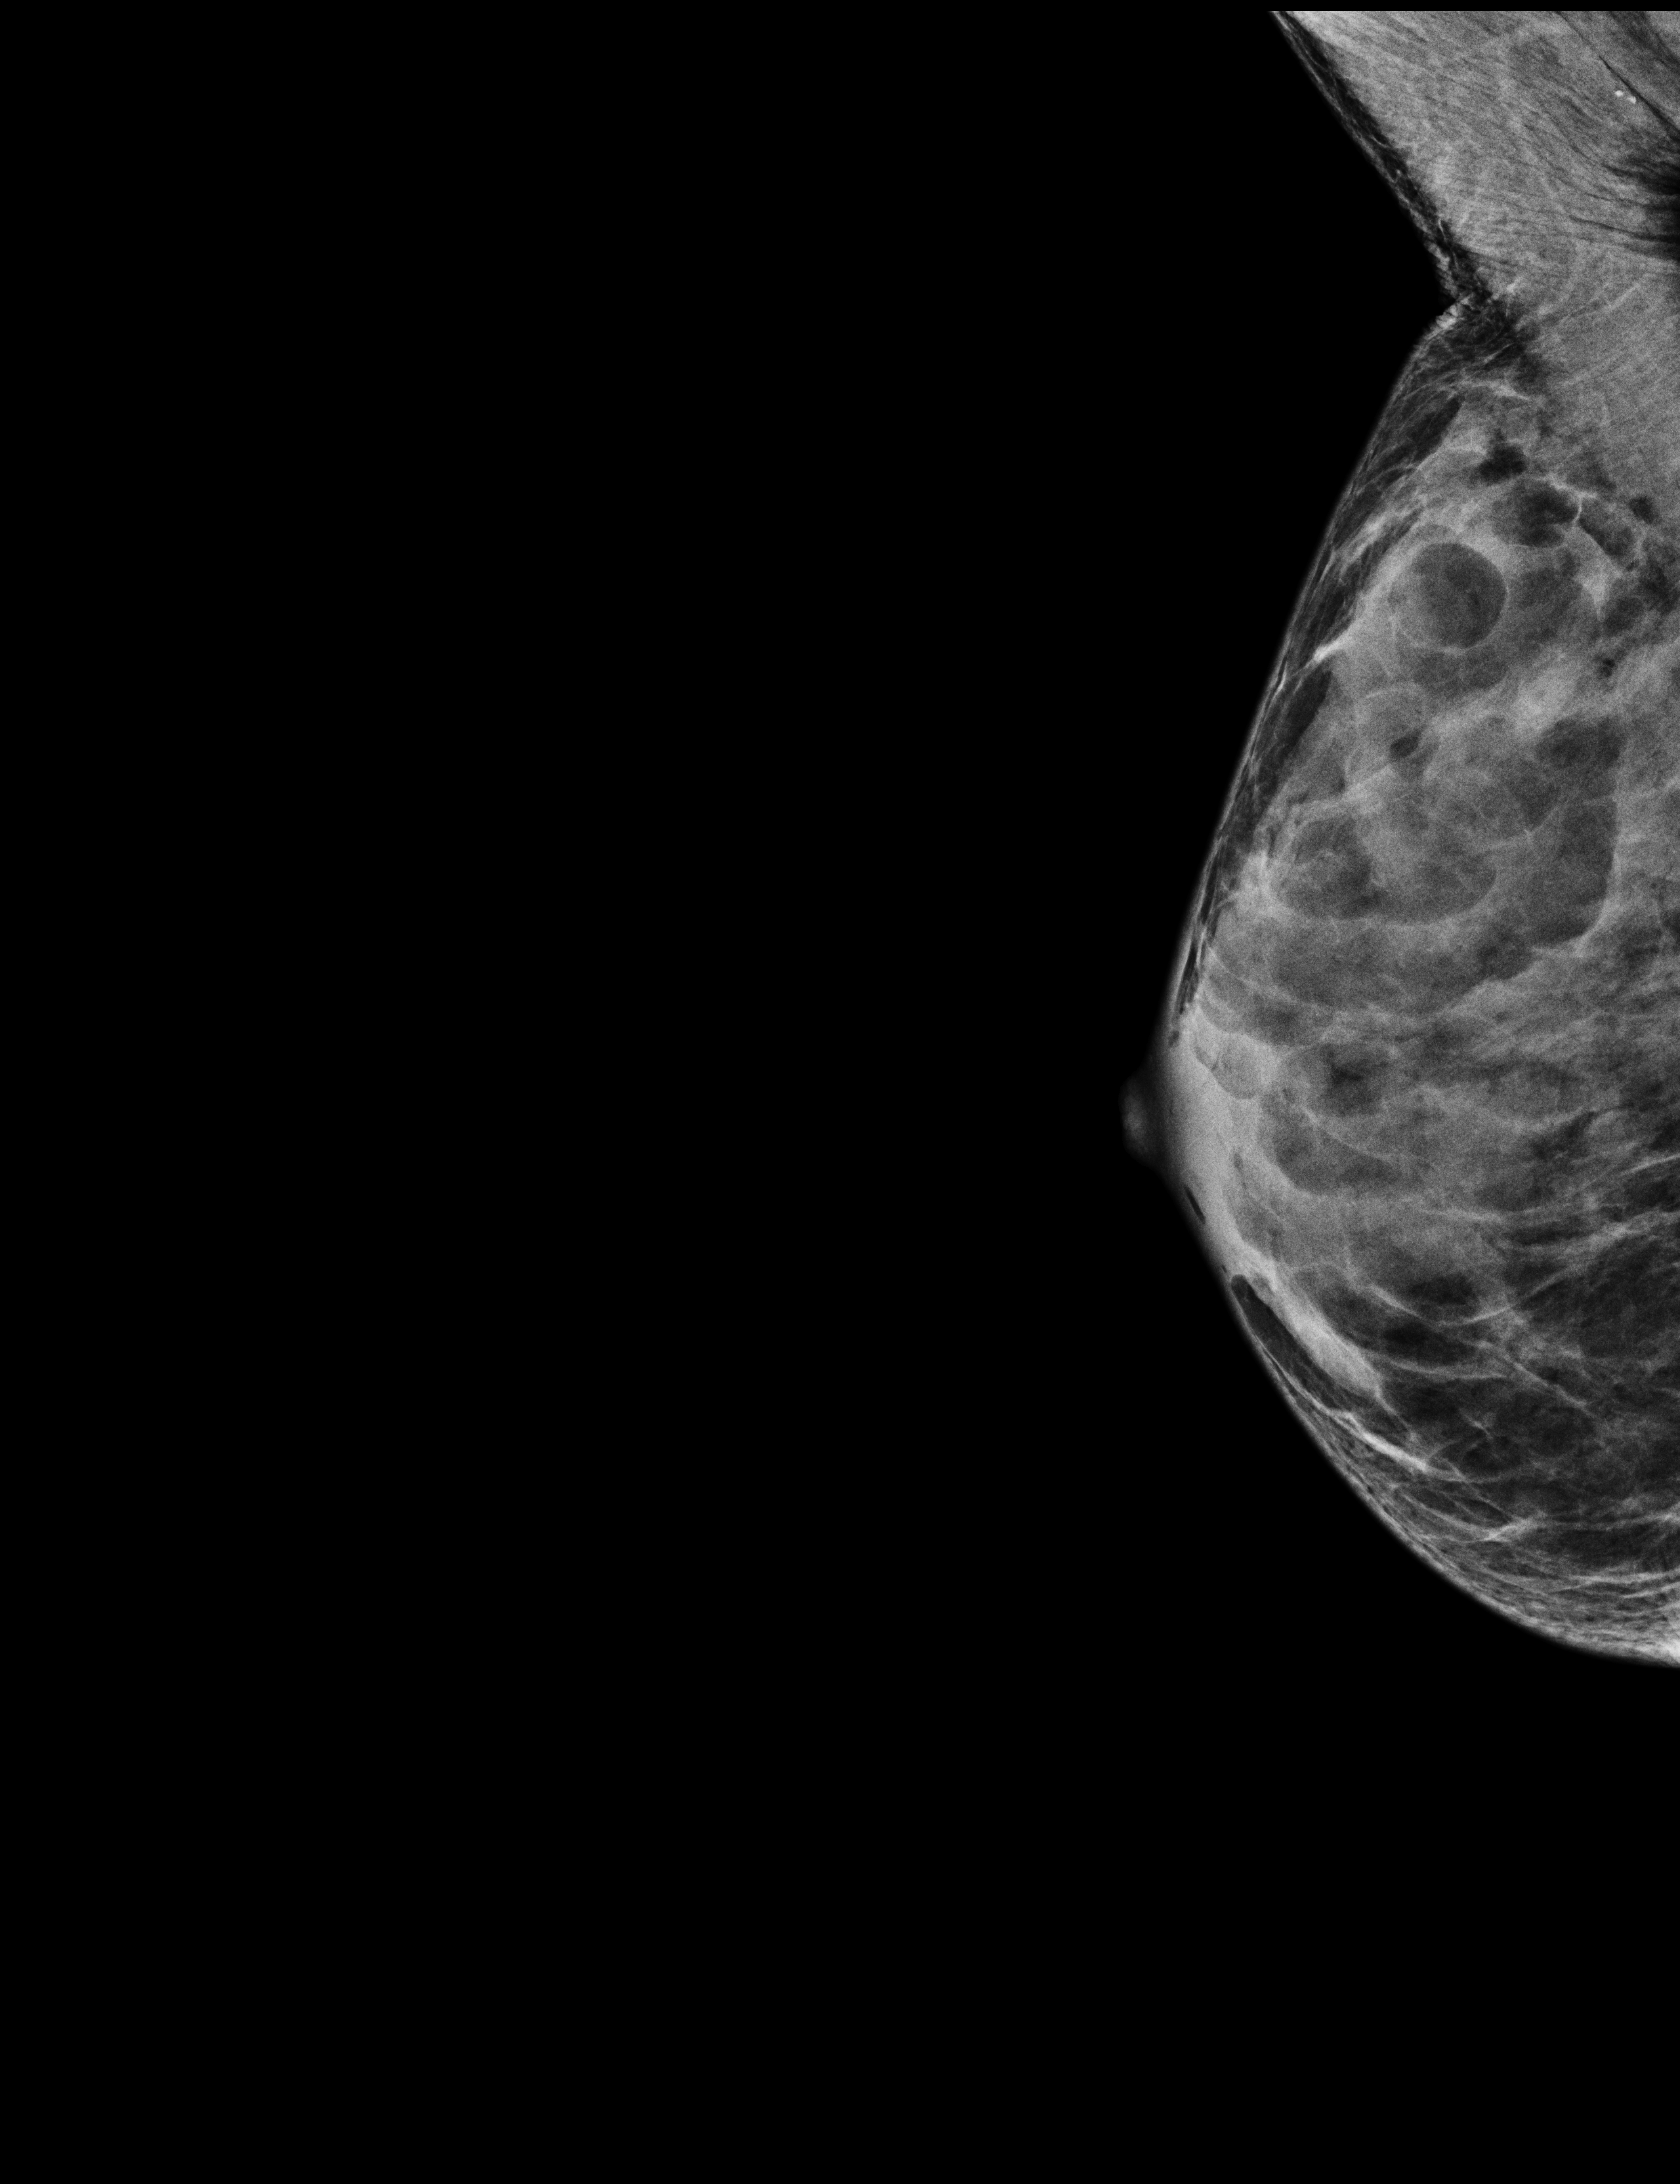
Screening examination; compressed breast thickness 22 mm. Patient: female, 69 years.
Image type: full-field digital mammogram. Breast: right. Projection: MLO view.